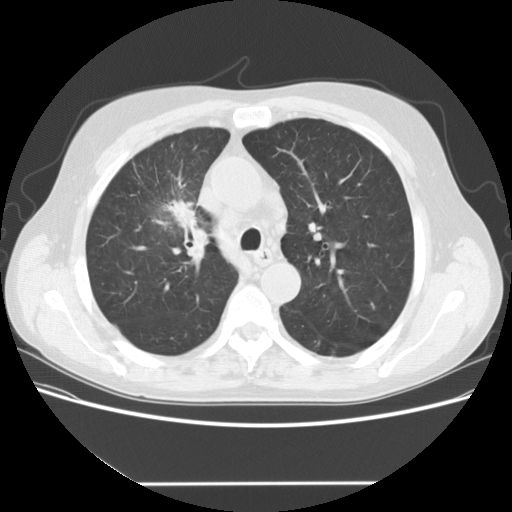
Low-dose screening chest CT, one axial slice; slice 107 of 153 in the series (ordered by position); reconstruction kernel STANDARD; lung window (W 1500 / L -600 HU); 2.5 mm slice thickness; 512 × 512 image matrix.
Structures marked on this image (expert manual segmentation):
- lesion 1 (tumor, upper lobe of right lung): bounding box <162,199,198,229> (left, top, right, bottom; pixels)